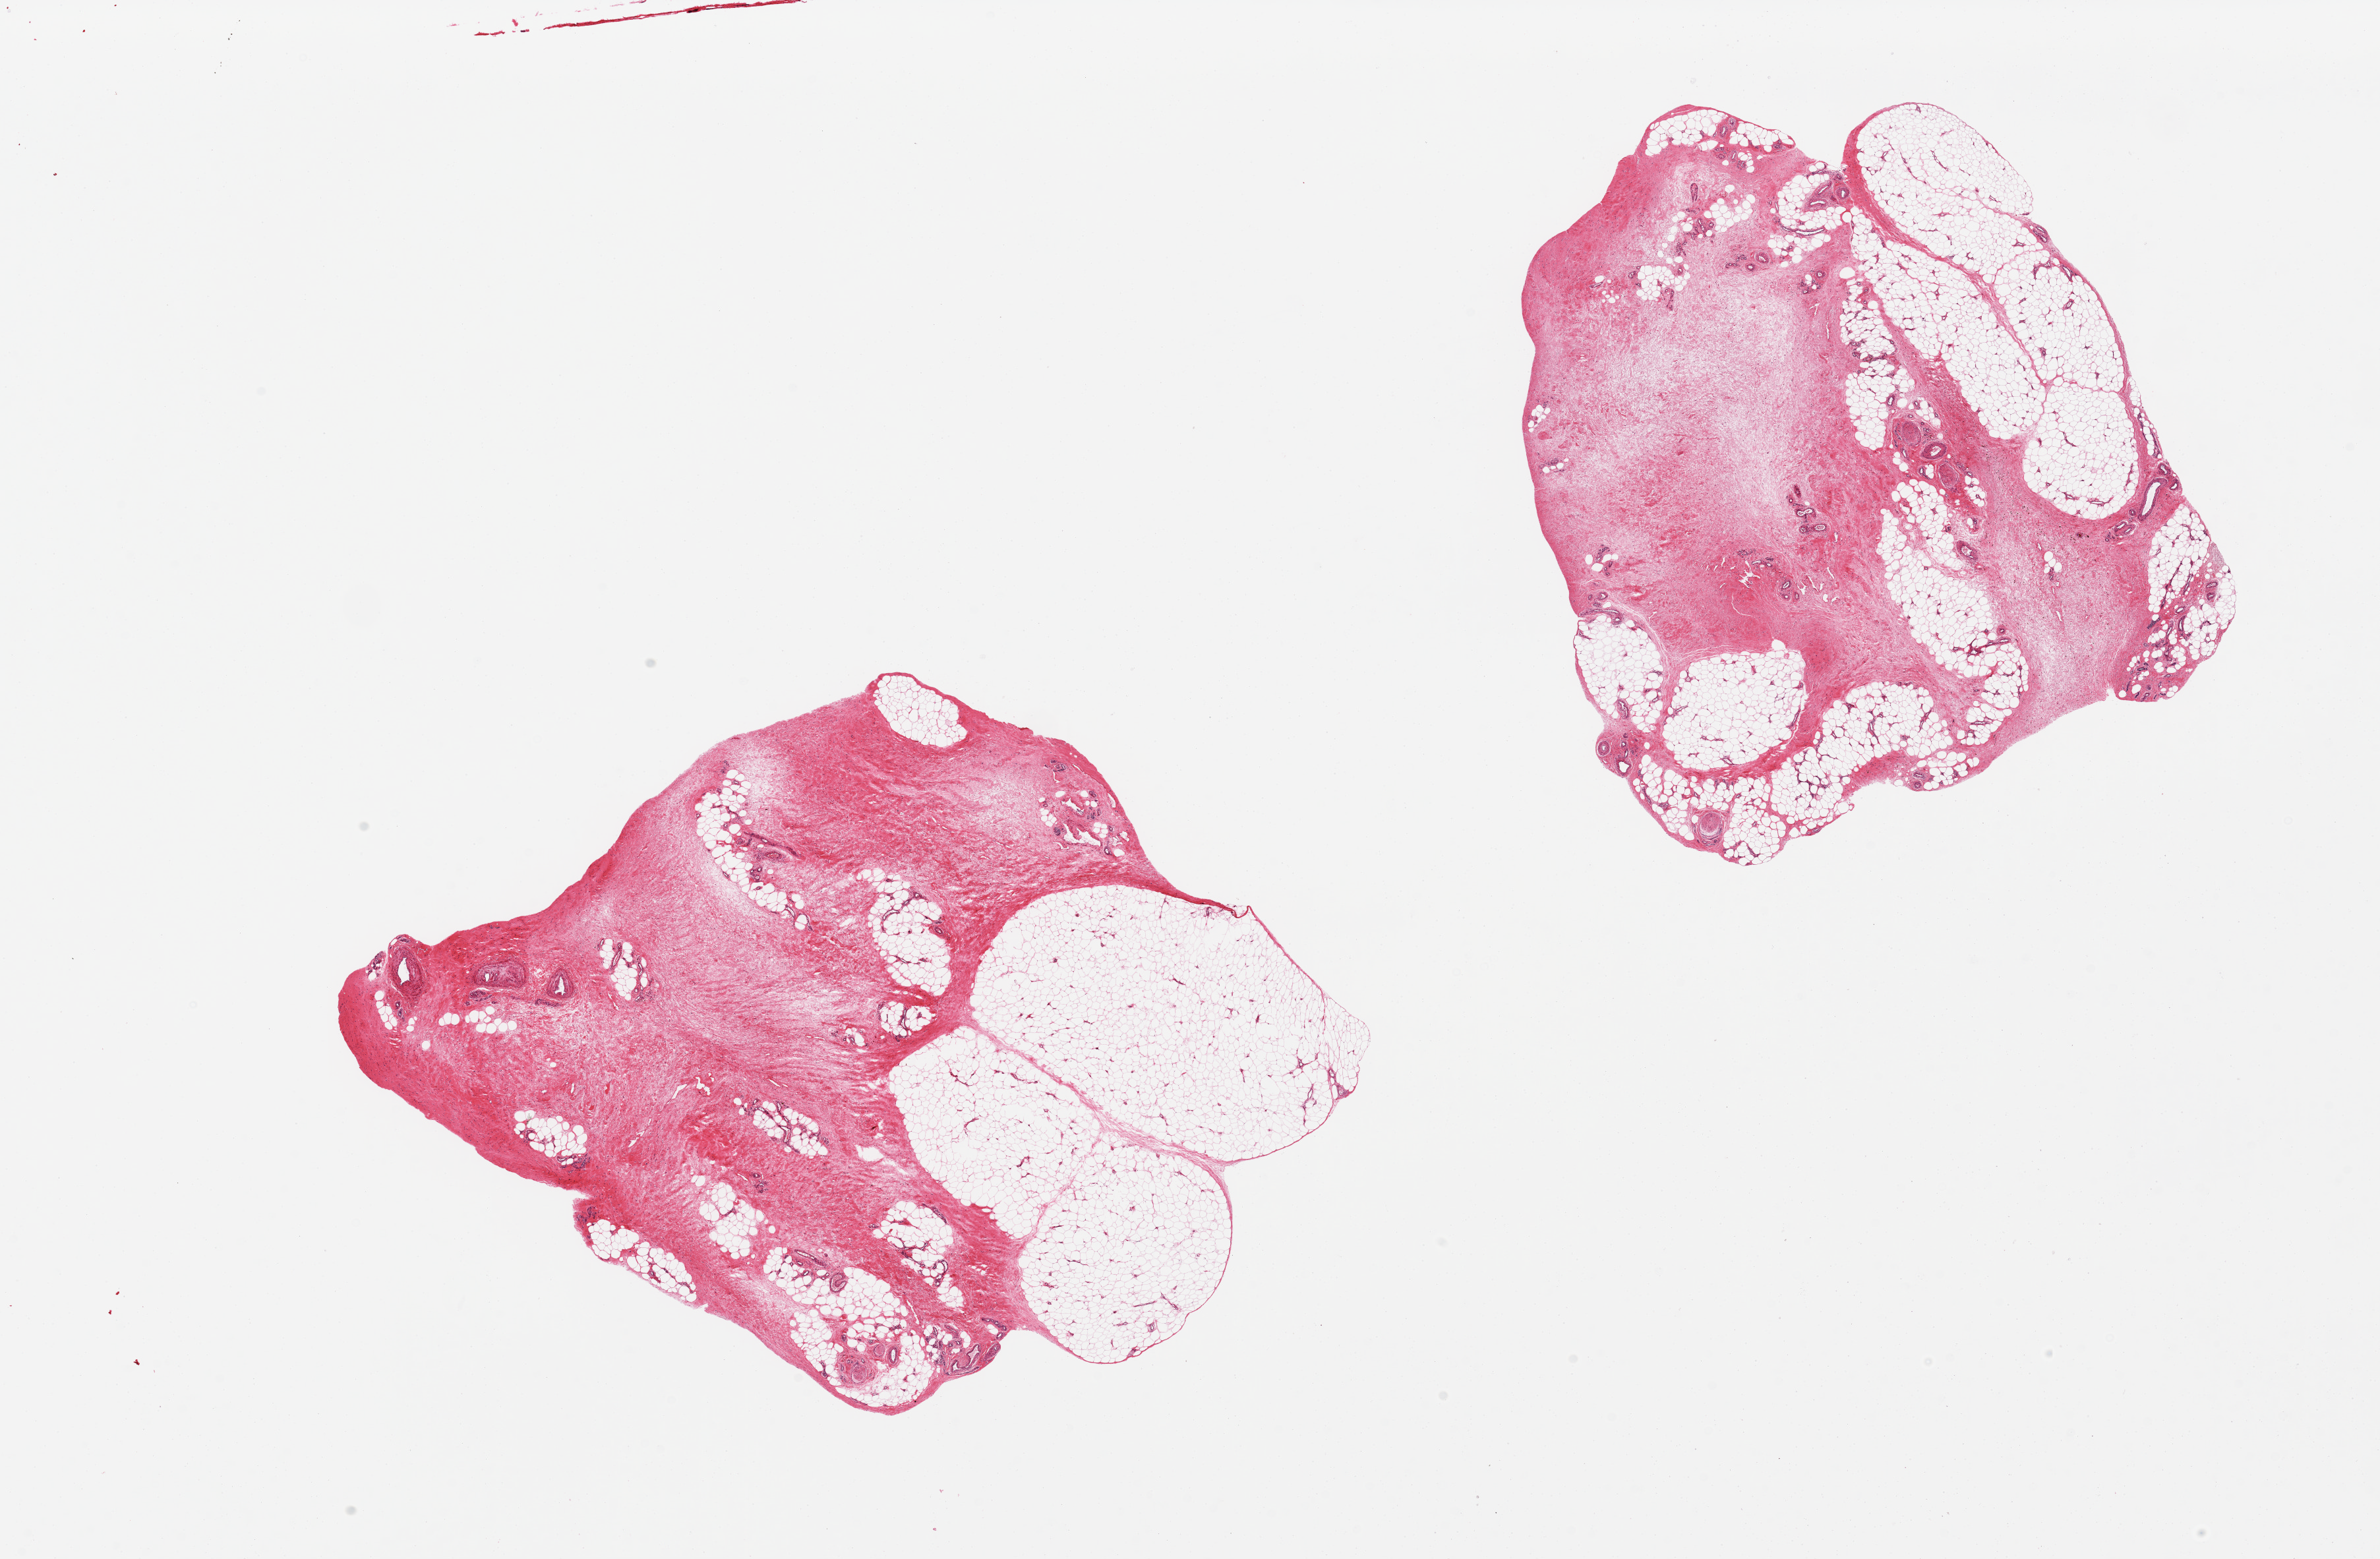
Digitized haematoxylin and eosin-stained section — whole scanned area (about 28.5 x 18.7 mm) shown as a low-resolution overview, PAXgene-fixed paraffin-embedded (PFPE) section, target tissue: adipose tissue, donor tissue sample. Male donor.
Pathologist's review note for this sample: 2 pieces, 40-50% adipose tissue, rest is fibroconnective tissue.